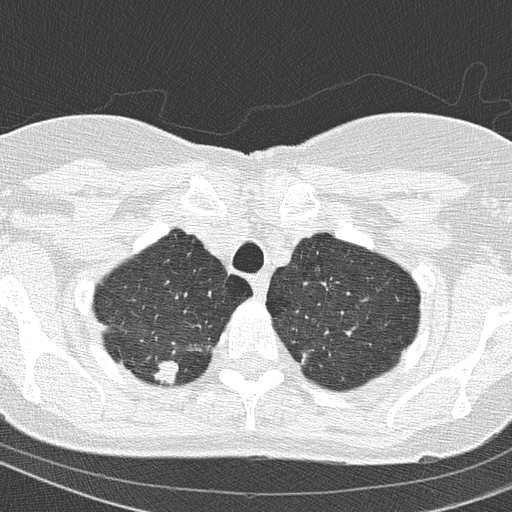
Low-dose screening chest CT, one axial slice; position 133 of 154 along the scan axis; 120 kVp; lung window (W 1500 / L -600 HU); 2 mm slice thickness; 512 × 512 image matrix, field of view 288 × 288 mm.
Structures marked on this image (outlined manually by an expert reader):
- lesion 1 (tumor, upper lobe of right lung): bounding box (x1, y1, x2, y2) in pixels: (154, 361, 179, 386)